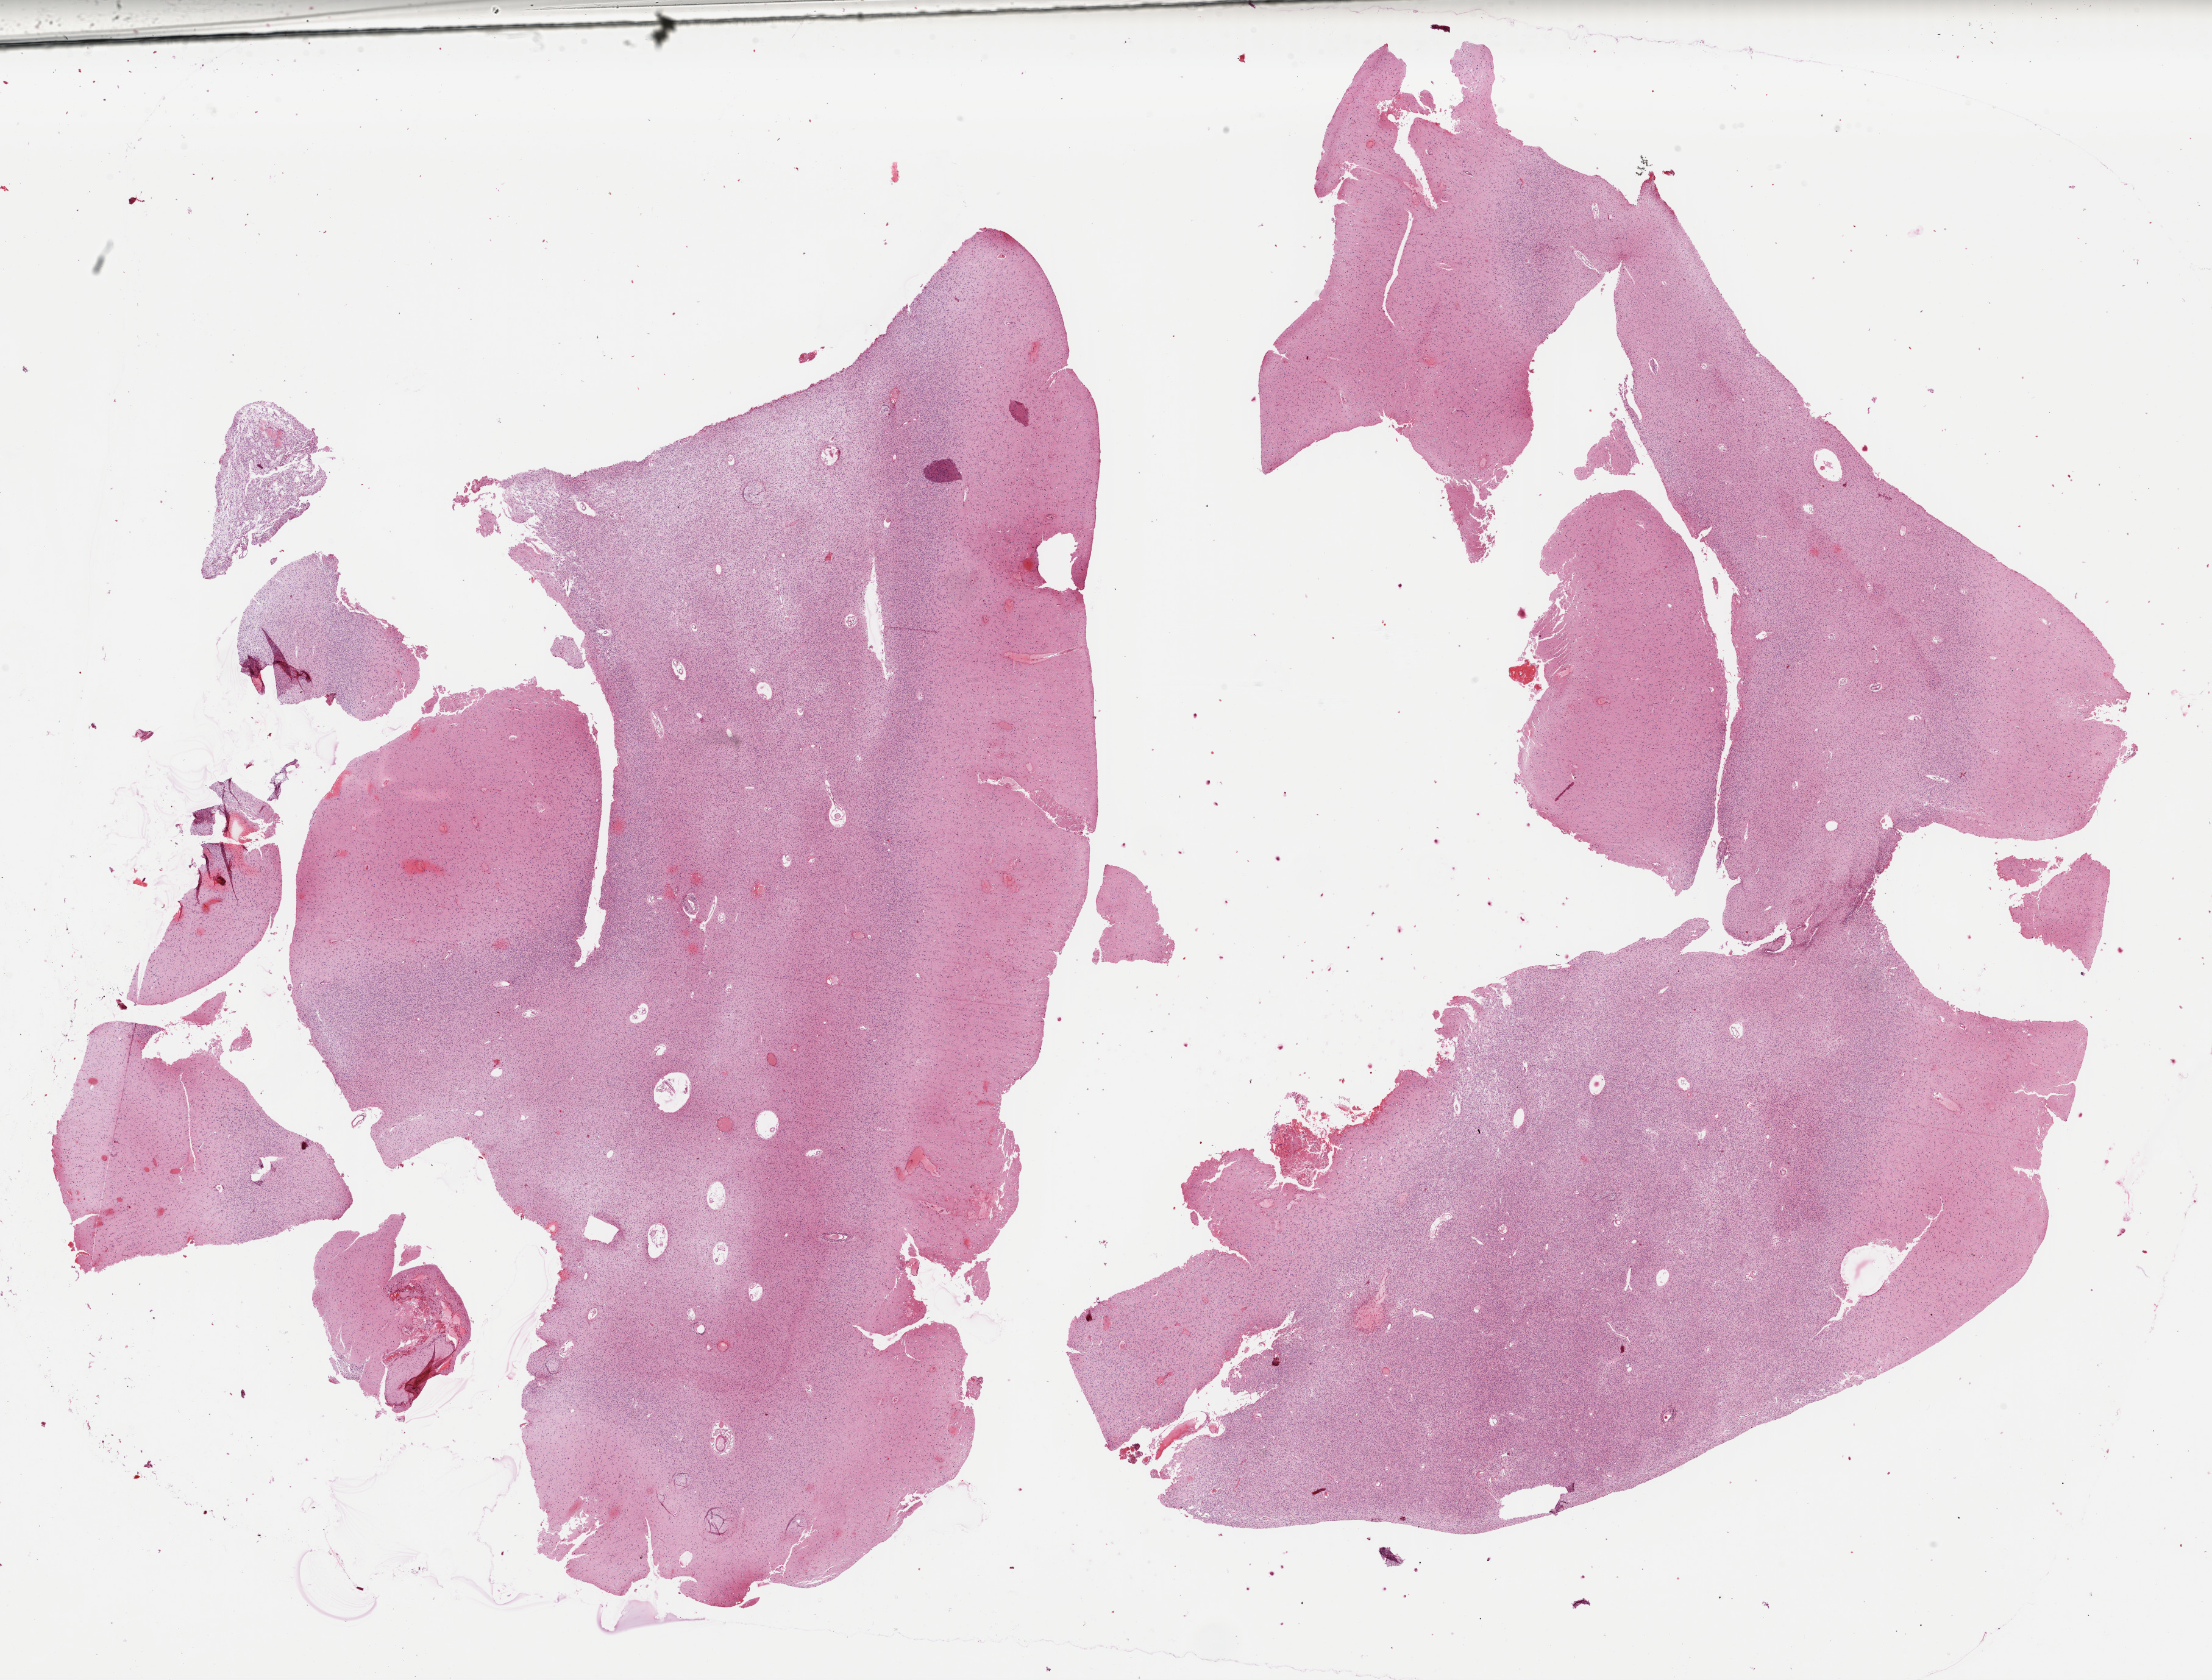
H&E-stained whole-slide image, shown as a low-resolution overview of the whole scanned area (about 28.6 x 21.8 mm). FFPE section. Primary tumour sample from the brain. Male, age 38 years at initial diagnosis. Histologic grade: G3 (poorly differentiated).
• histologic diagnosis: Mixed glioma
• laterality: right